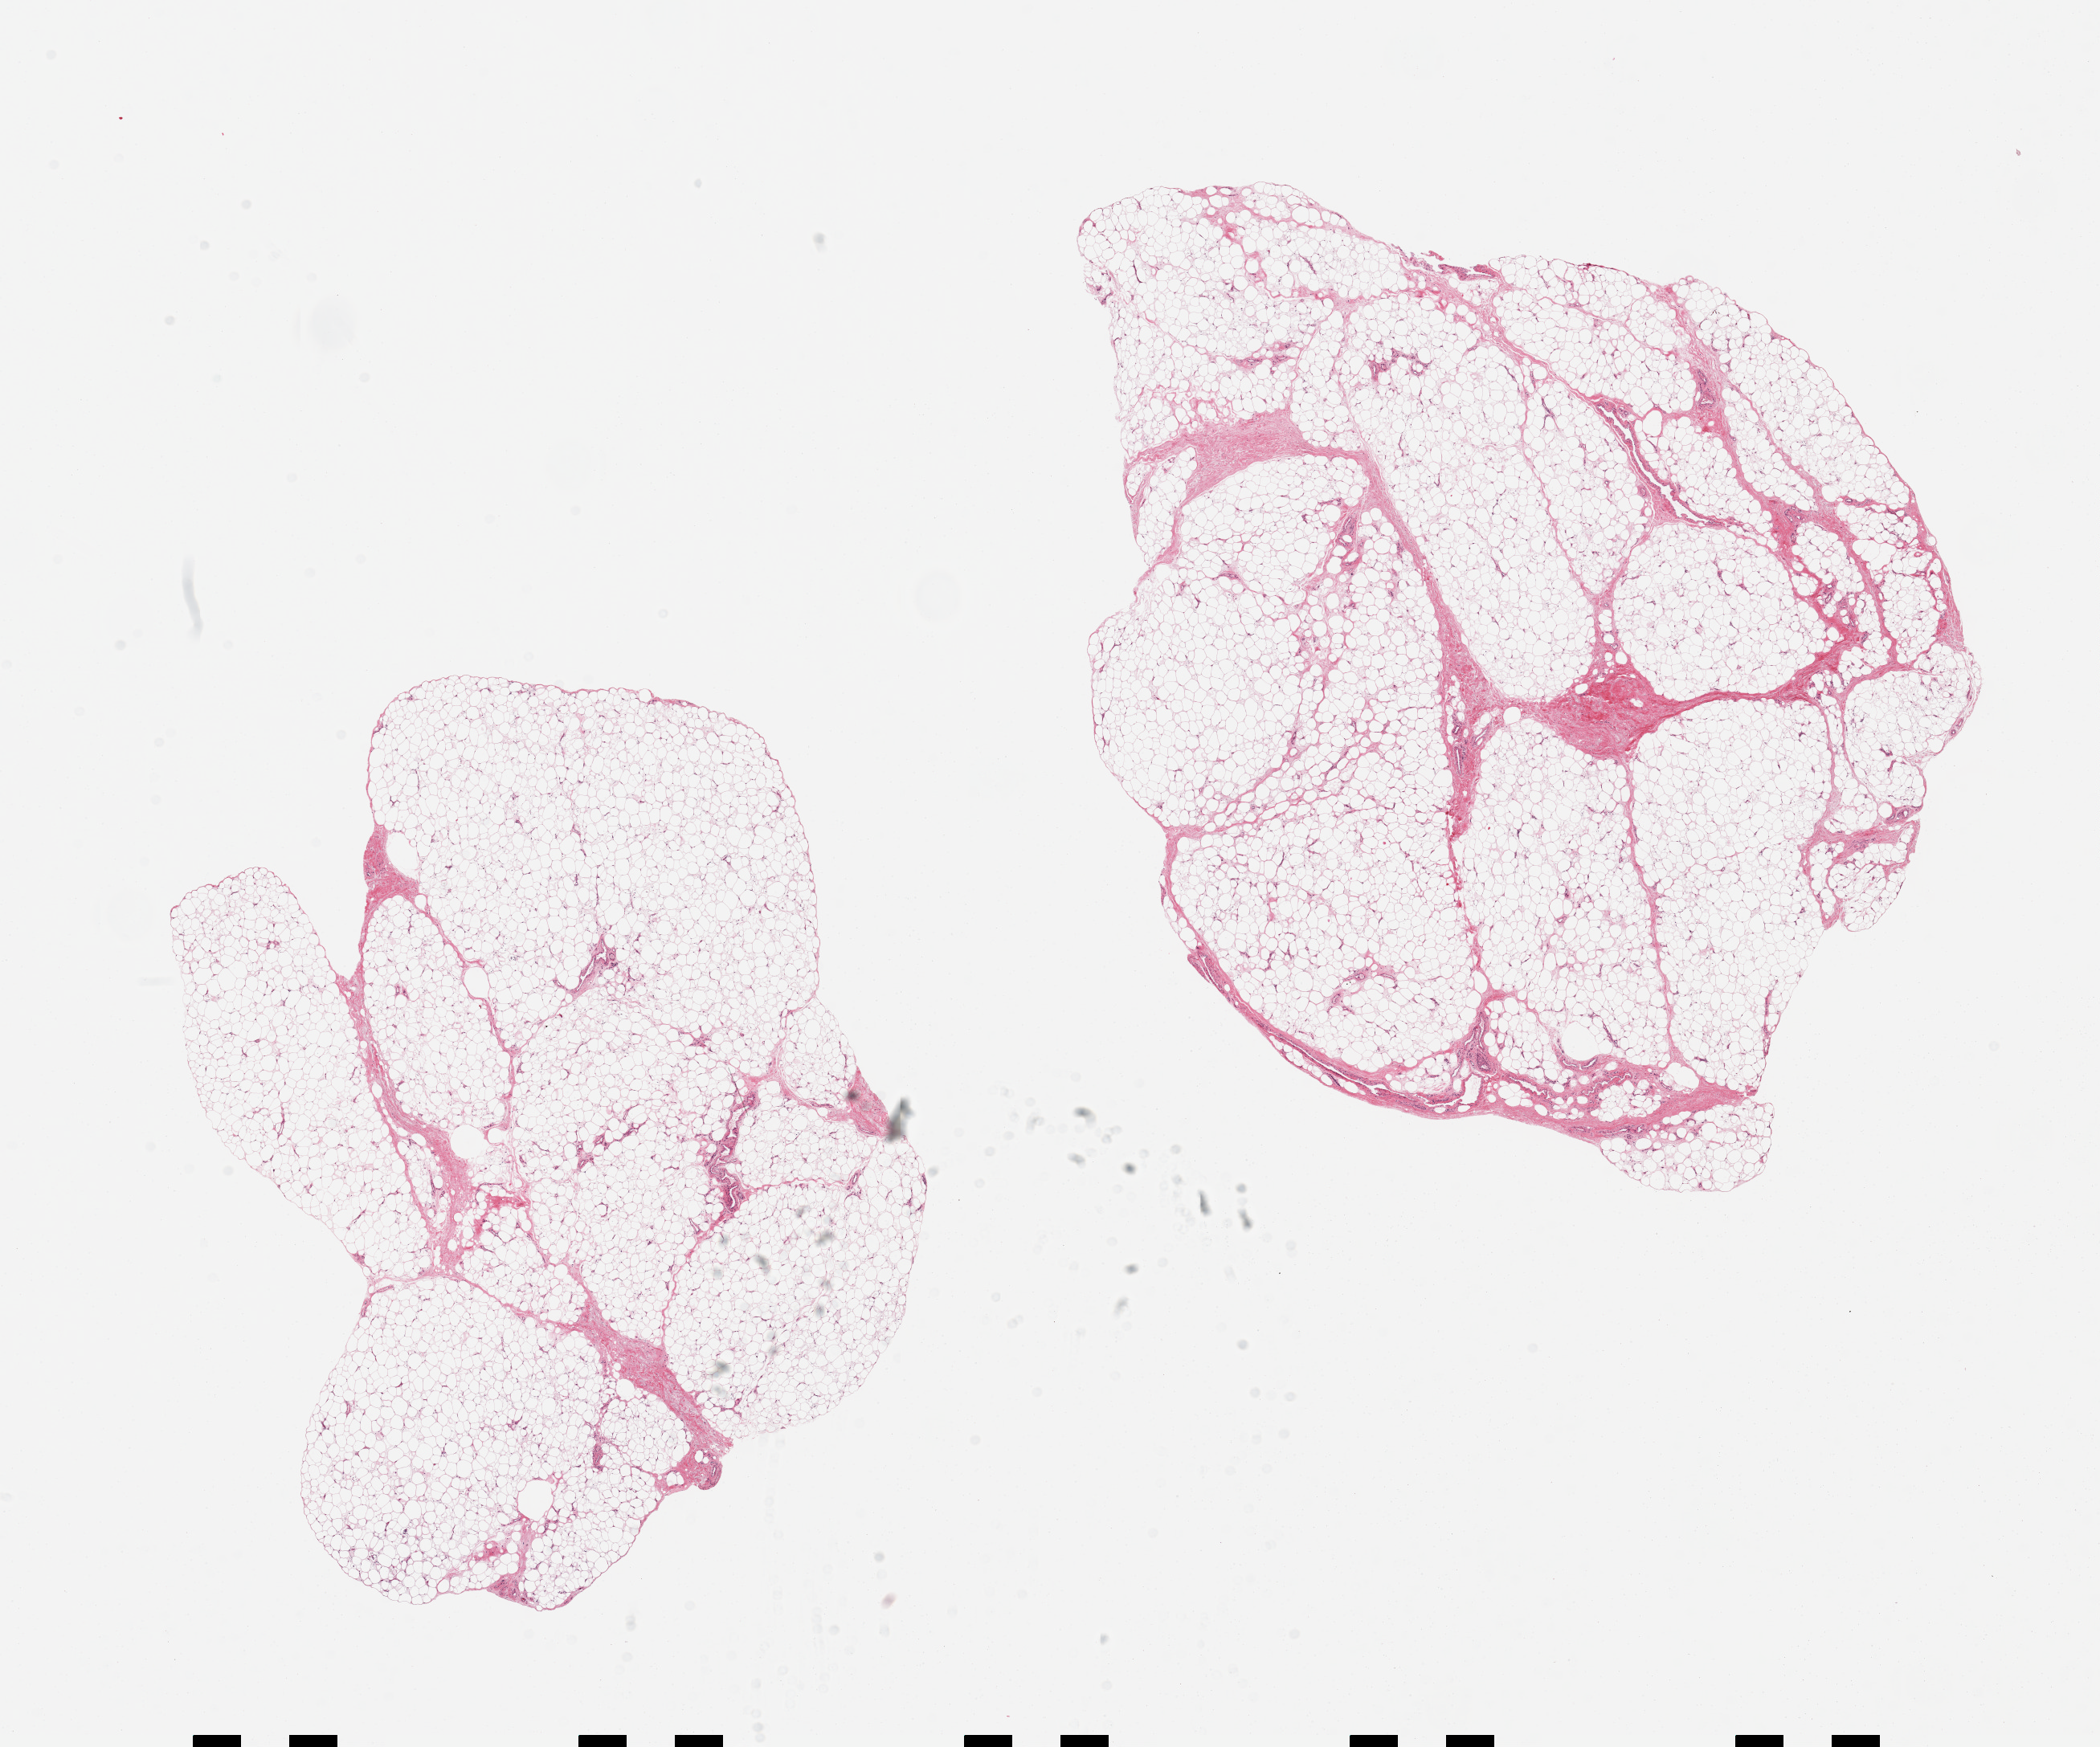
H&E whole-slide image — whole scanned area (about 20.7 x 17.2 mm) shown as a low-resolution overview. PAXgene-fixed paraffin-embedded (PFPE) section. Section of adipose tissue (target tissue). Tissue donor sample.
Reviewer comment on this tissue sample: 2 pieces, ~10-15% fibro-fascial tisssue.